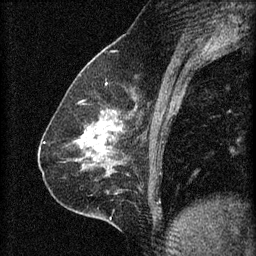
Breast MRI (dynamic contrast-enhanced), one sagittal slice. Position 27 of 60 along the scan axis. 3 images stored at this slice position (order not interpretable as contrast timing). 1.5 T. TE 4.2 ms, TR 8.2 ms. 2 mm slice thickness. 256 × 256 image matrix, field of view 180 × 180 mm. Female patient, age 59 years.
Annotated regions visible in this slice (semi-automatic segmentation, software-assisted and operator-edited):
- analysis volume of interest (the breast-tissue region the enhancement analysis was run in; not a lesion): box from (x=62, y=104) to (x=129, y=161) px
- tumour enhancement mask (voxels above the 70 % enhancement threshold inside the analysis volume of interest): (x=79, y=120)–(x=112, y=151)